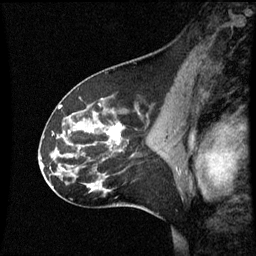
Breast MRI (dynamic contrast-enhanced), one sagittal slice; slice 34 of 60 in the series (ordered by position); dynamic contrast-enhanced series, image 2 of 3 at this slice position (ordered by acquisition); 1.5 T; TE 4.2 ms, TR 8.9 ms; 2 mm slice thickness; 256 × 256 image matrix, field of view 200 × 200 mm. Female patient, age 45 years. Case-level facts recorded for this patient, not image findings: setting: breast cancer imaged before/during neoadjuvant chemotherapy; receptor status: HR-positive, HER2-negative.
Structures marked on this image (semi-automatically segmented with operator editing):
- analysis volume of interest (the breast-tissue region the enhancement analysis was run in; not a lesion): bounding box <46,94,171,205> (left, top, right, bottom; pixels)
- tumour enhancement mask (voxels above the 70 % enhancement threshold inside the analysis volume of interest): <68,104,125,145>